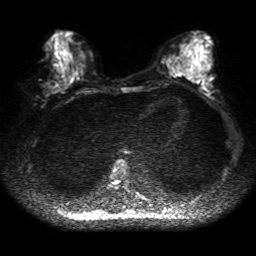
Breast MRI, one axial slice; slice 19 of 50 in the series (ordered by position); diffusion-weighted series; image 2 of 4 stored at this slice position (different b-values; order by instance number); 1.5 T; 4 mm slice thickness; 256 × 256 image matrix. Female patient.
Outlined on this slice (manually delineated by an expert):
- tumour on diffusion-weighted imaging: box from (x=47, y=82) to (x=61, y=93) px